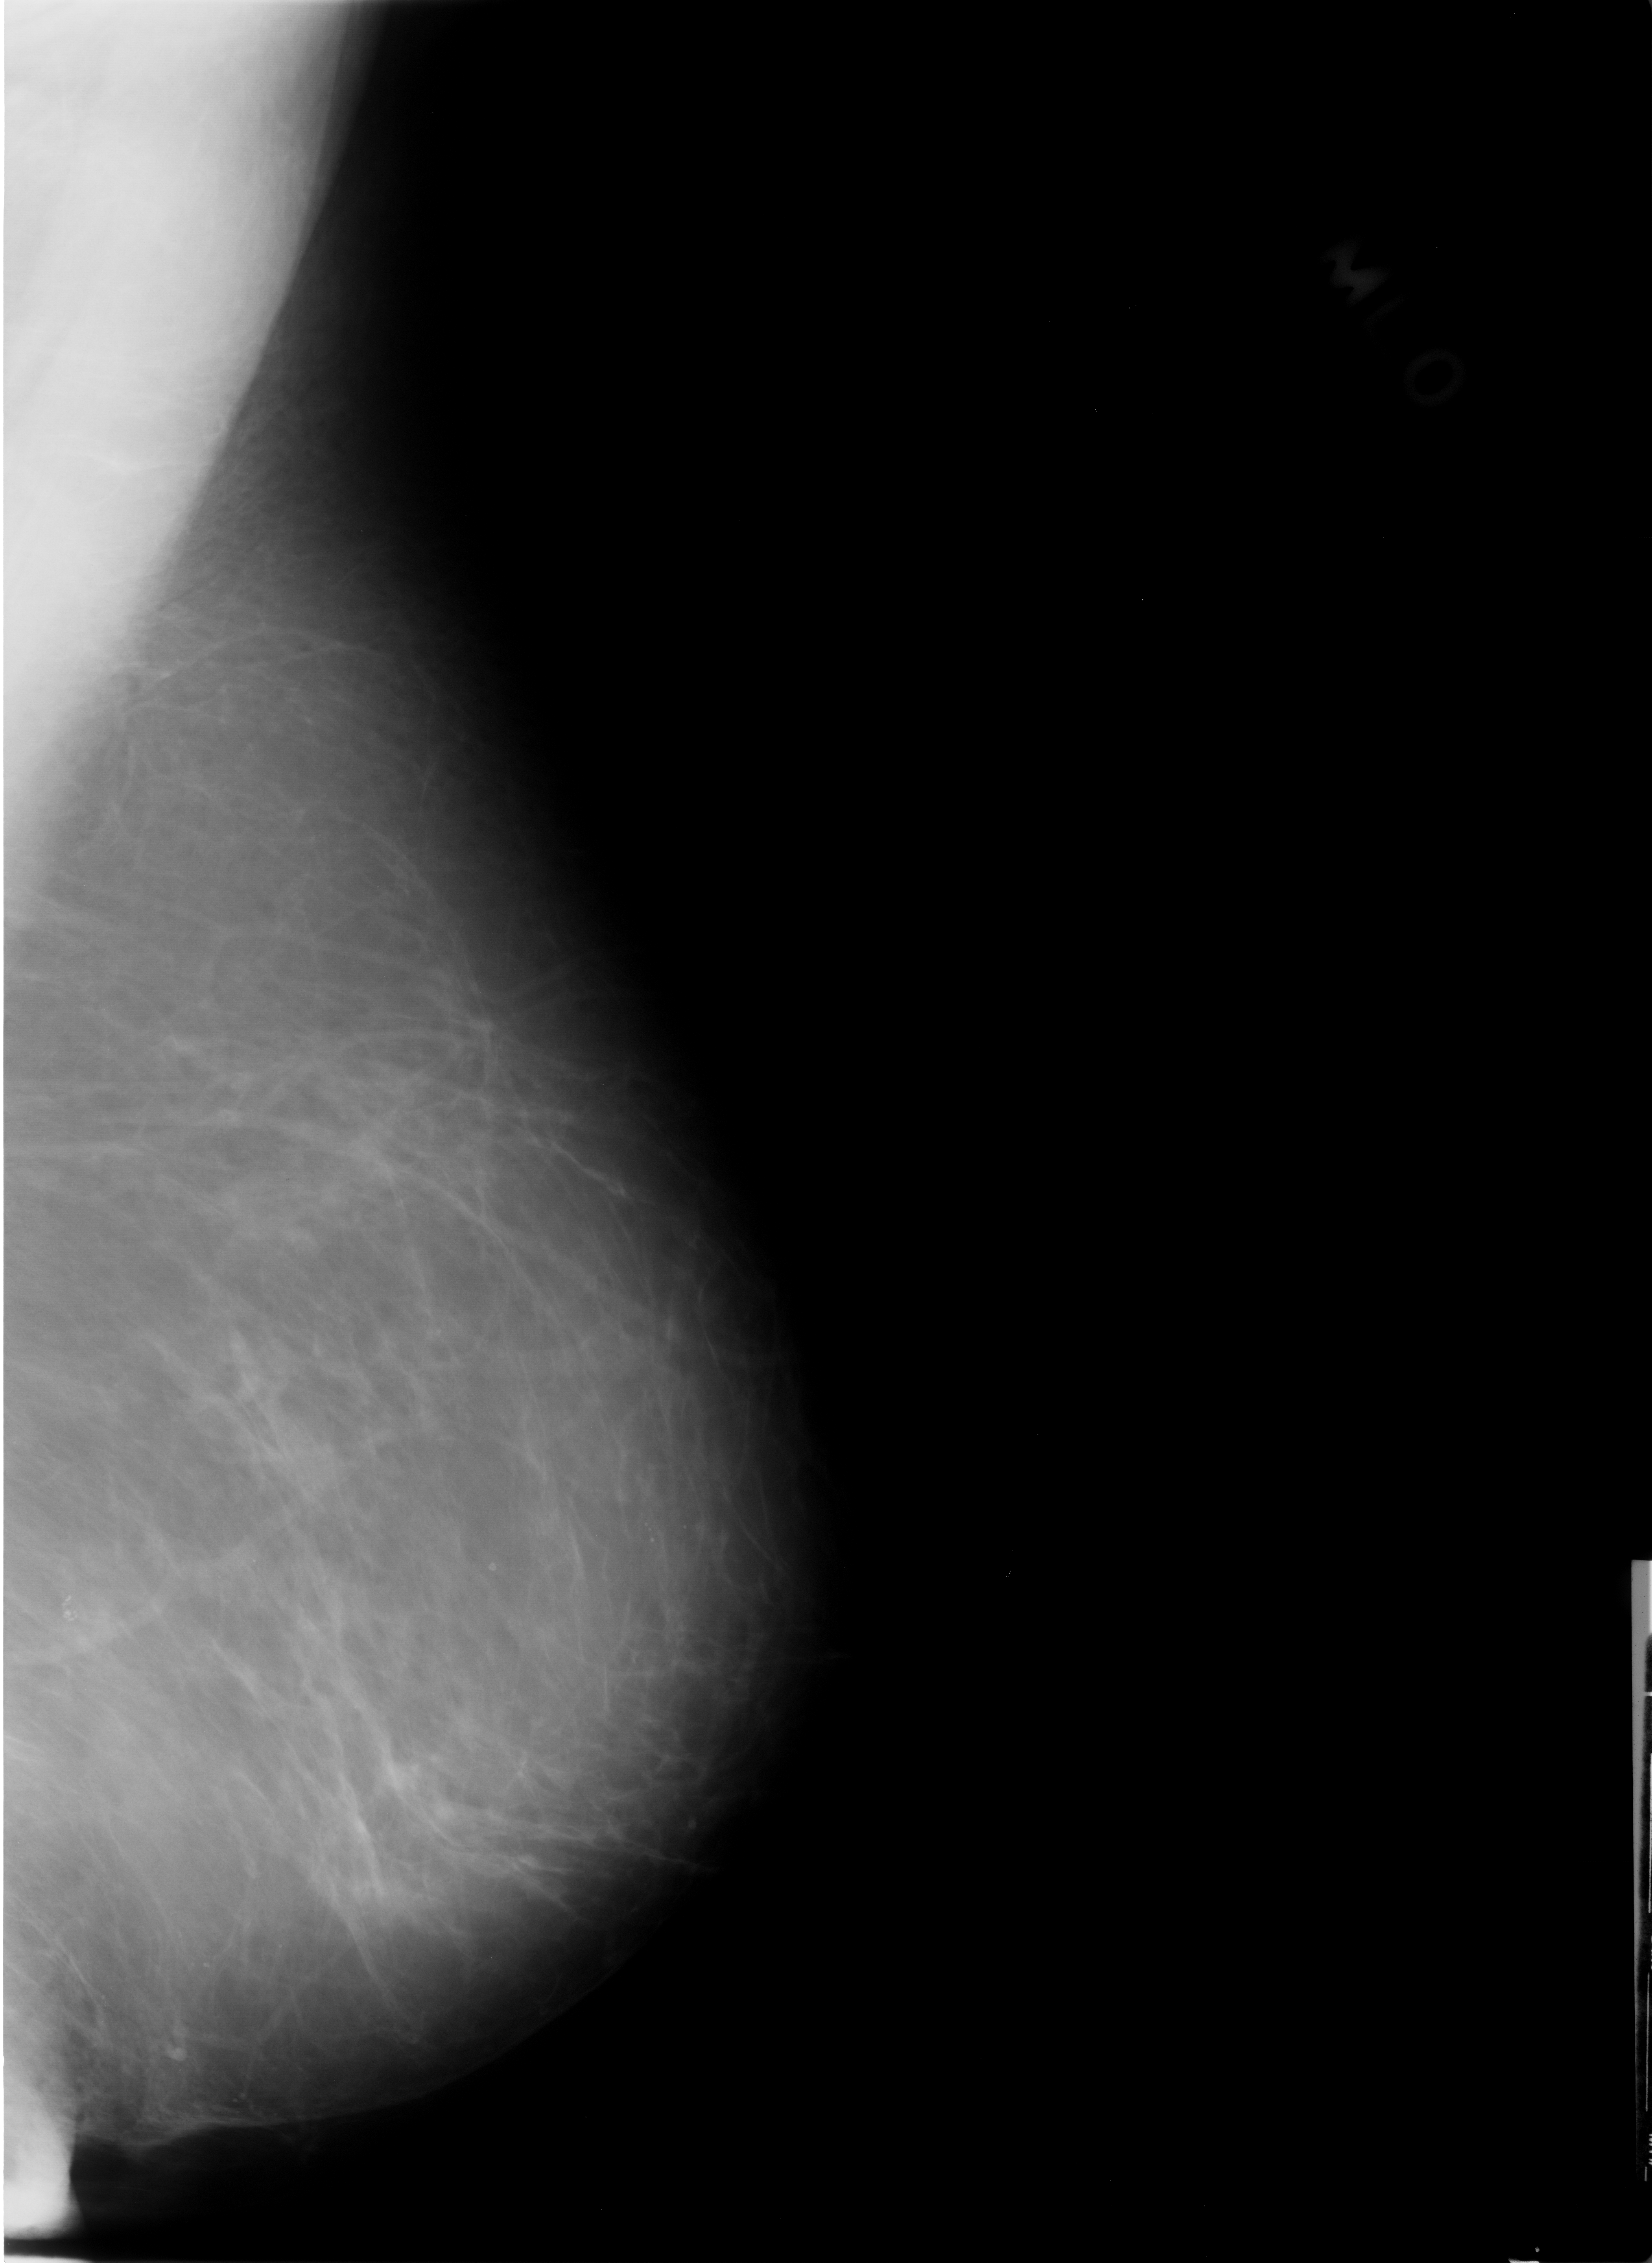
Digitized screen-film mammogram, left breast, mediolateral oblique (MLO) view, BI-RADS breast density category 1 (scale 1–4).
- Calcifications, morphology pleomorphic, distribution clustered; BI-RADS assessment category 4; pathology (as recorded): benign.